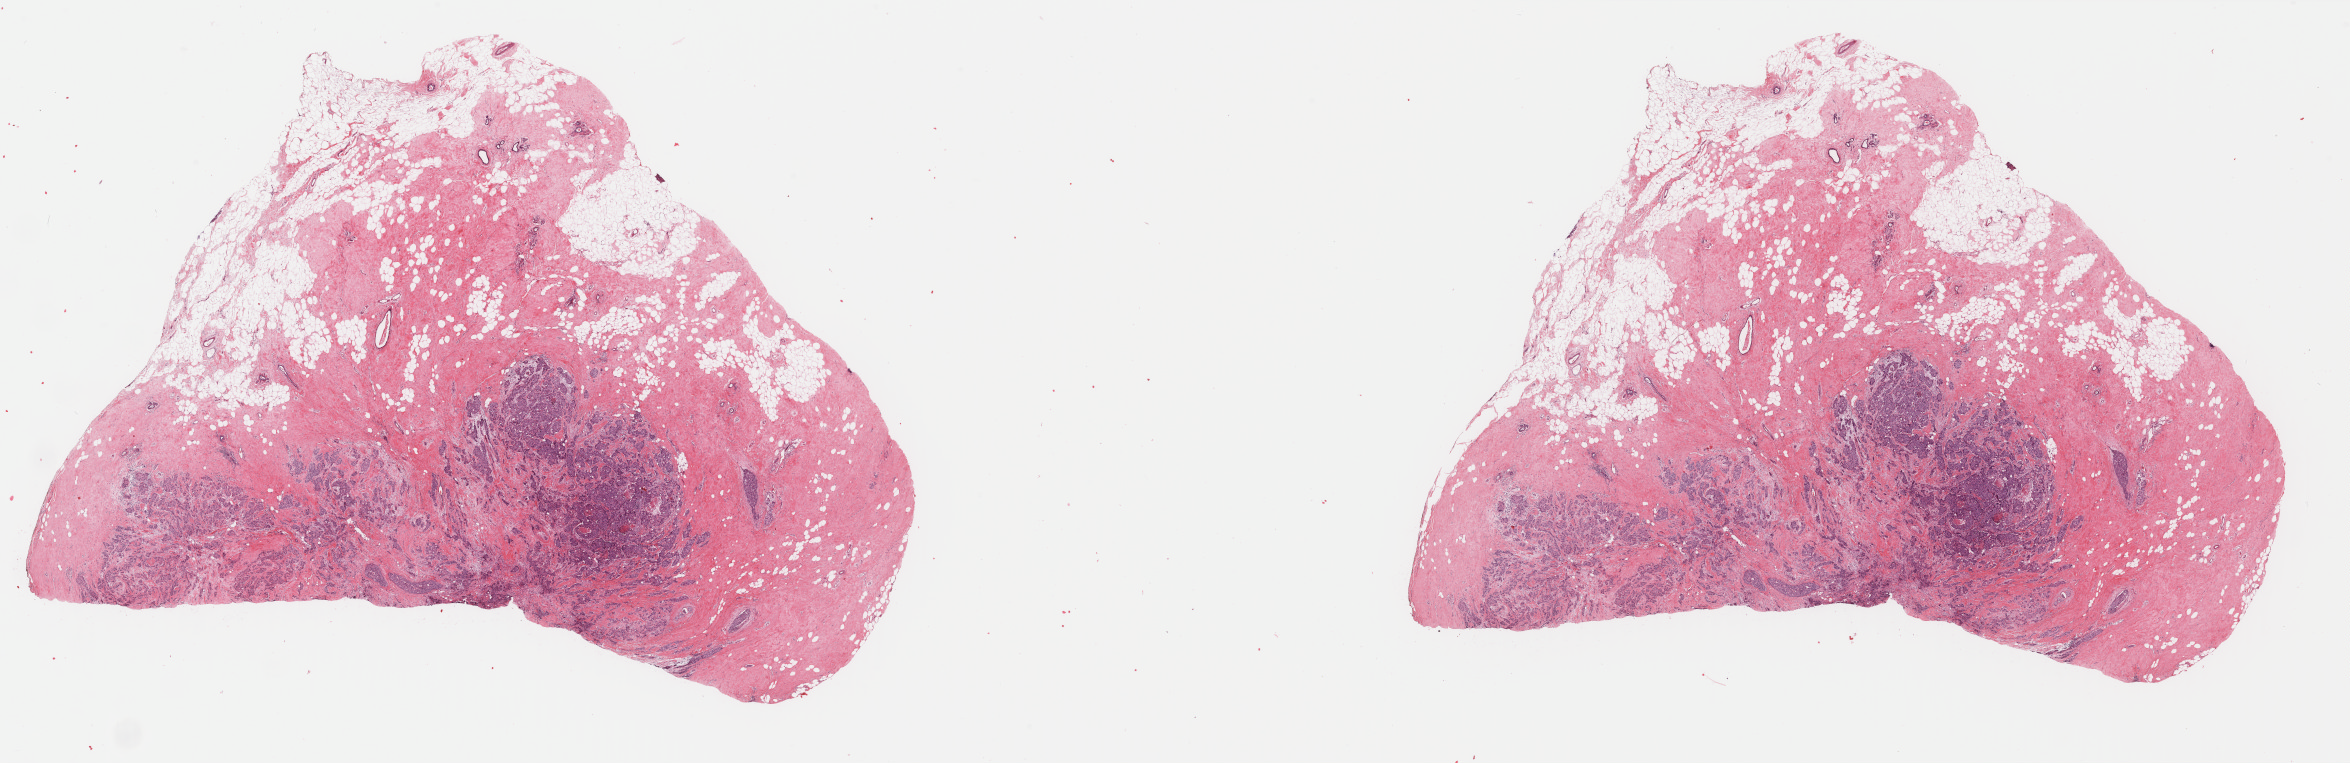
Digitized Hematoxylin and eosin (H&E) stained tissue section (whole slide), shown as a low-resolution overview of the whole scanned area (about 37.3 x 12.1 mm, acquisition: 40x scan); formalin-fixed paraffin-embedded (FFPE) diagnostic section; breast, primary tumour sample. Female, age 70 years at initial diagnosis.
Lymph nodes positive (case pathology): 5 of 17 examined. Diagnosis: Infiltrating duct carcinoma, NOS. AJCC pathologic stage: IIIA (7th edition).